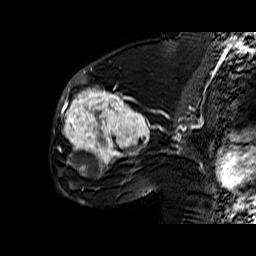
Breast MRI (dynamic contrast-enhanced), one sagittal slice. Position 33 of 60 along the scan axis. Dynamic contrast-enhanced series, time point 2 of 6 at this slice position (early post-contrast). 1.5 T. TE 6.4 ms, TR 32.9 ms. 256 × 256 image matrix, field of view 200 × 200 mm. Female patient. From the clinical record (not read from this slice): setting: breast cancer imaged before/during neoadjuvant chemotherapy; receptor status: triple-negative.
Annotated regions visible in this slice (semi-automatic segmentation, software-assisted and operator-edited):
- analysis volume of interest (the breast-tissue region the enhancement analysis was run in; not a lesion): bounding box <55,65,159,174> (left, top, right, bottom; pixels)
- tumour enhancement mask (voxels above the 100 % enhancement threshold inside the analysis volume of interest): <58,73,150,174>